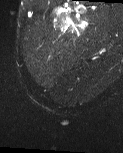
MRI of an extremity soft-tissue mass, one axial slice; position 5 of 60 along the scan axis; T2-weighted fat-saturated; MR volume resampled by the dataset authors to the PET/CT grid (not the native acquisition matrix); 123 × 153 image matrix, field of view 120 × 149 mm. Male patient. Case-level facts recorded for this patient, not image findings: histological type: pleiomorphic liposarcoma; grade: high; site of the primary tumour: left thigh.
Annotated regions visible in this slice (expert contour drawn on MRI and transferred to this co-registered scan by the dataset authors):
- gross tumour volume including surrounding oedema: bounding box [x1, y1, x2, y2] px = [59, 20, 87, 35]